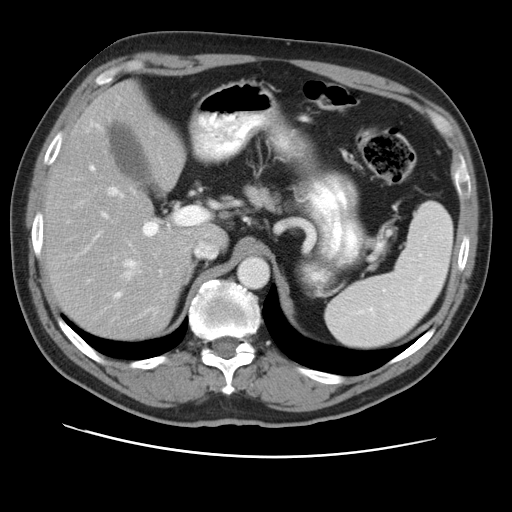
Contrast-enhanced abdominal CT, one axial slice. Position 31 of 49 along the scan axis. 120 kVp. Intravenous contrast given. Soft-tissue window (W 400 / L 40 HU). 512 × 512 image matrix, field of view 374 × 374 mm. Male patient, age 59 years. Case-level facts recorded for this patient, not image findings: diagnosis: colorectal cancer liver metastases, imaged before liver resection; multiple liver metastases: yes; largest metastasis: 6.3 cm.
Outlined on this slice (expert manual segmentation):
- hepatic veins: bounding box (x1, y1, x2, y2) in pixels: (109, 187, 215, 269)
- liver: (46, 85, 224, 341)
- planned liver remnant (the part of the liver to remain after resection): (46, 85, 223, 341)
- portal vein (with intrahepatic branches): (89, 164, 208, 297)